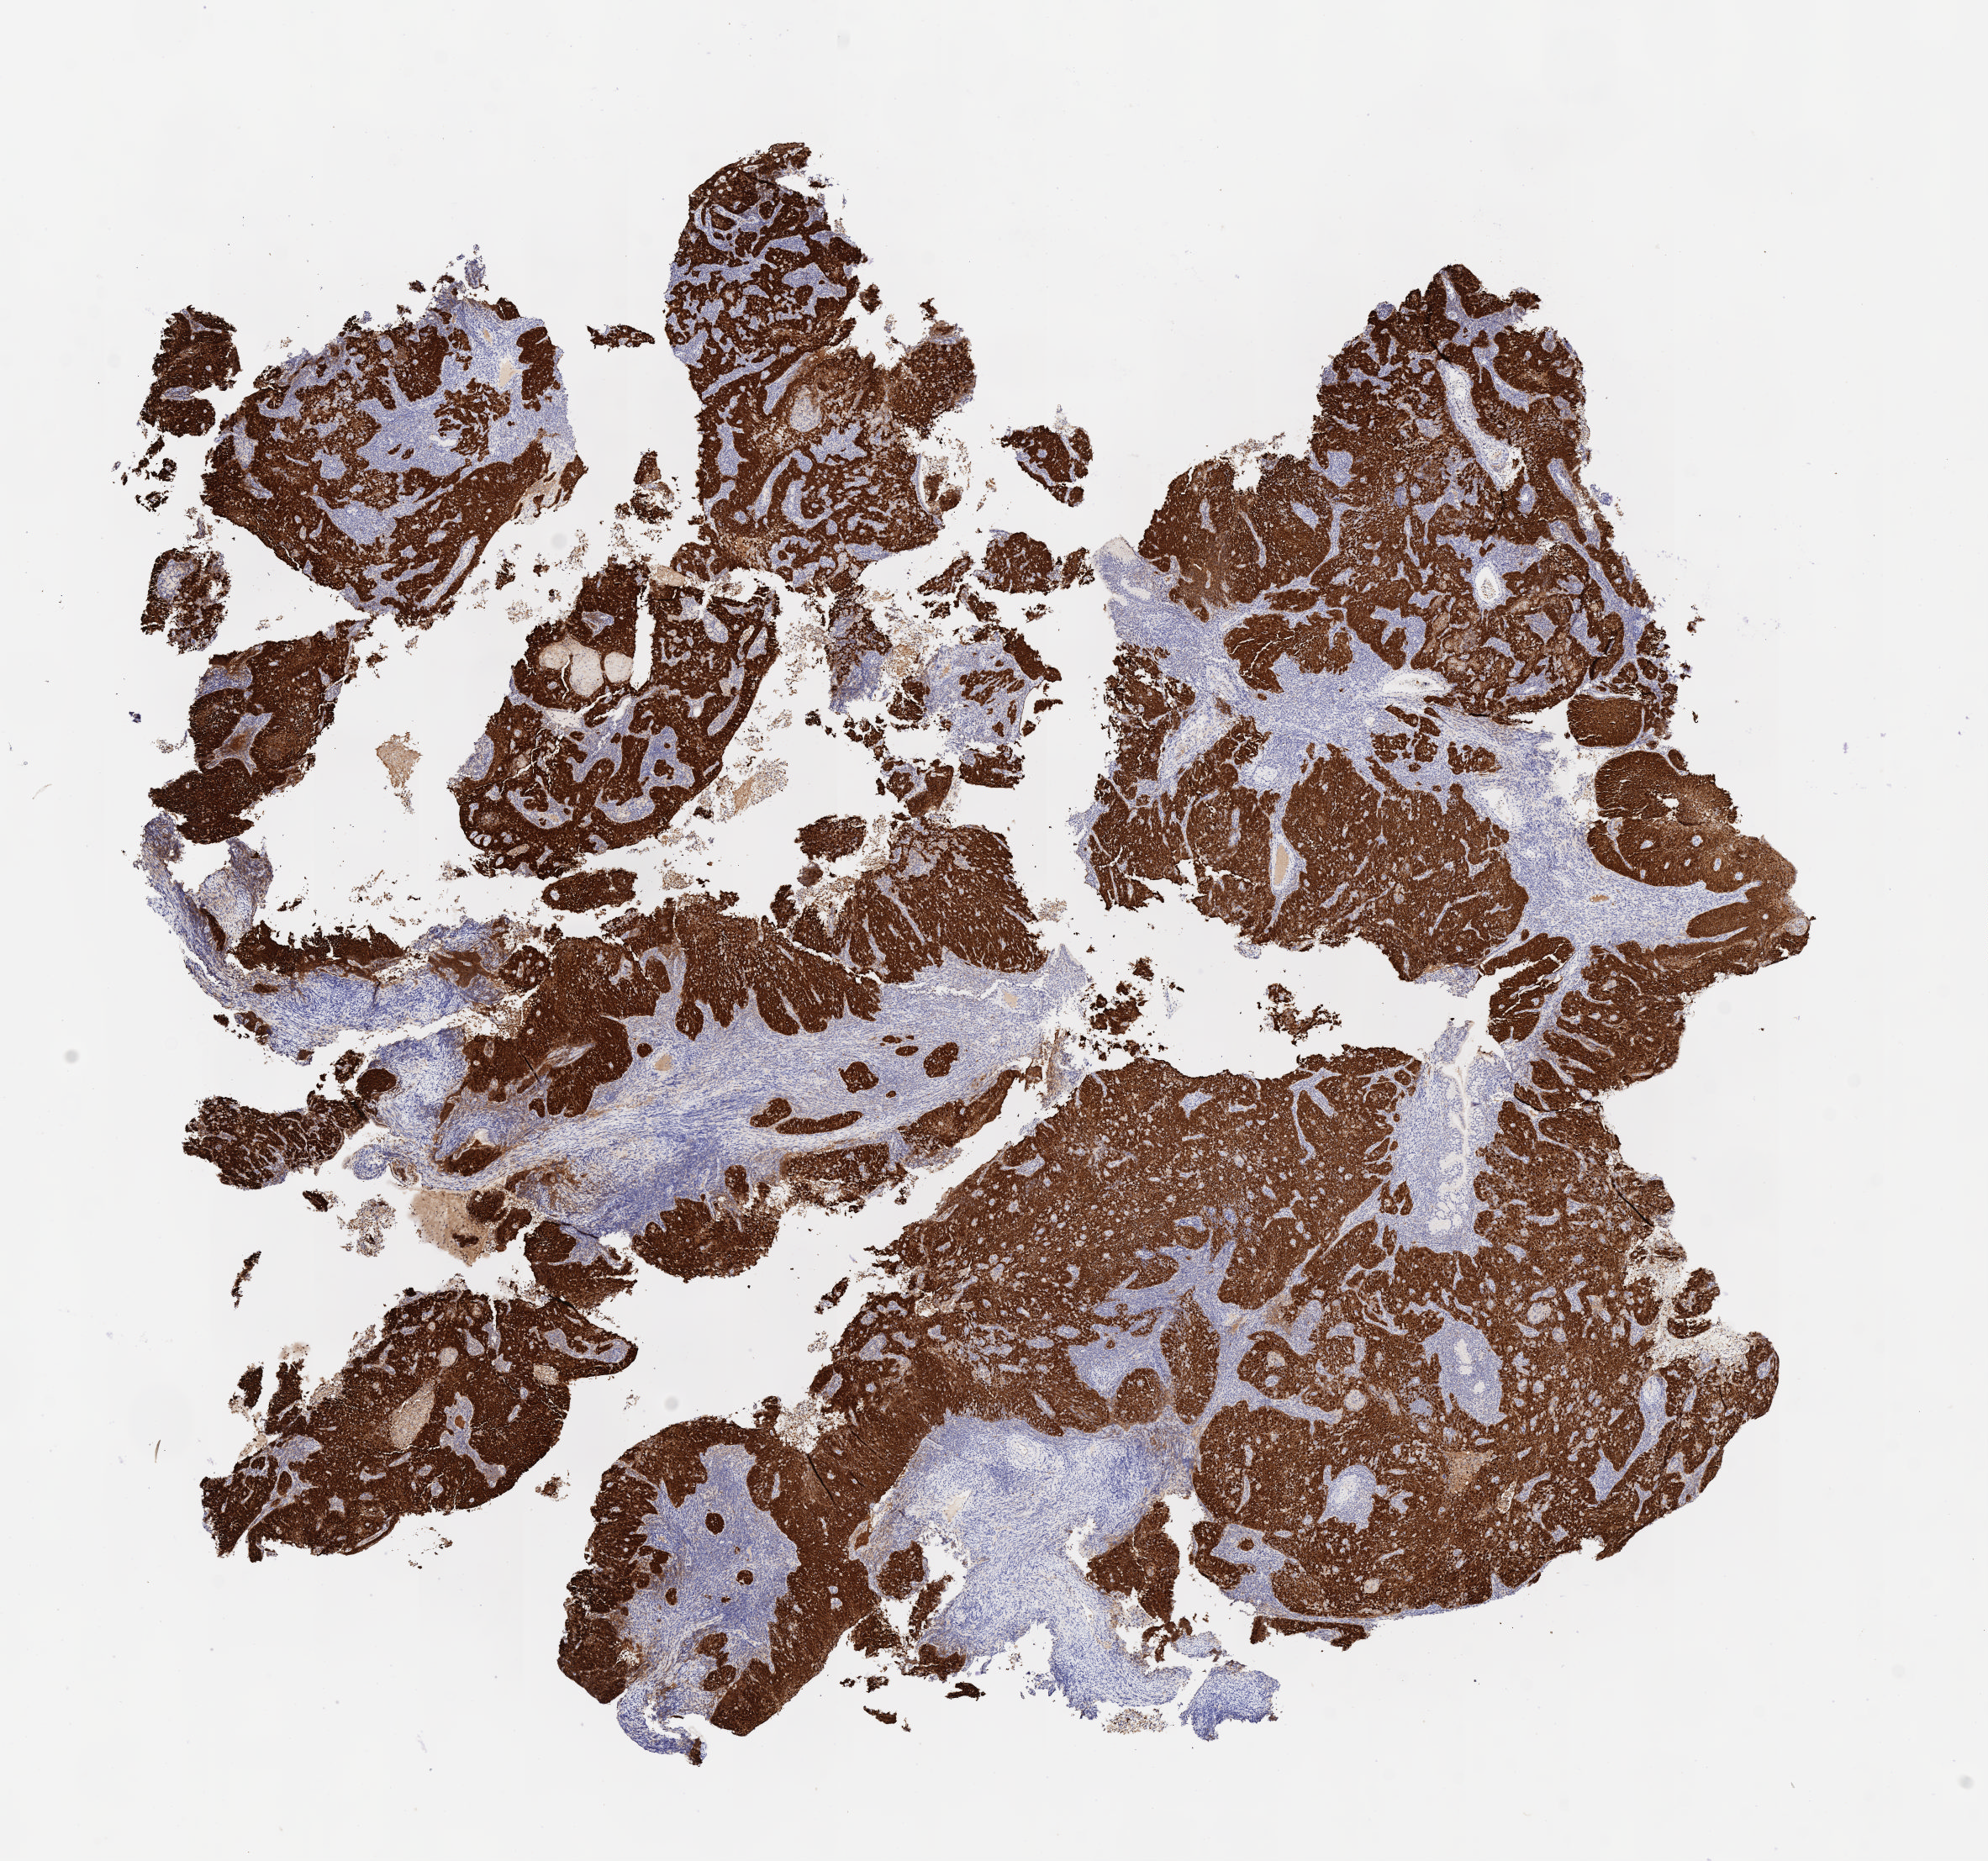
Immunohistochemistry (IHC) whole-slide image stained for p16 (p16INK4a), a low-resolution overview of the entire scanned area, about 9.6 x 8.9 mm, specimen: tumor tissue, site: cervix. Patient female; 37 years old.
Diagnosis: Lymphoepithelial carcinoma.